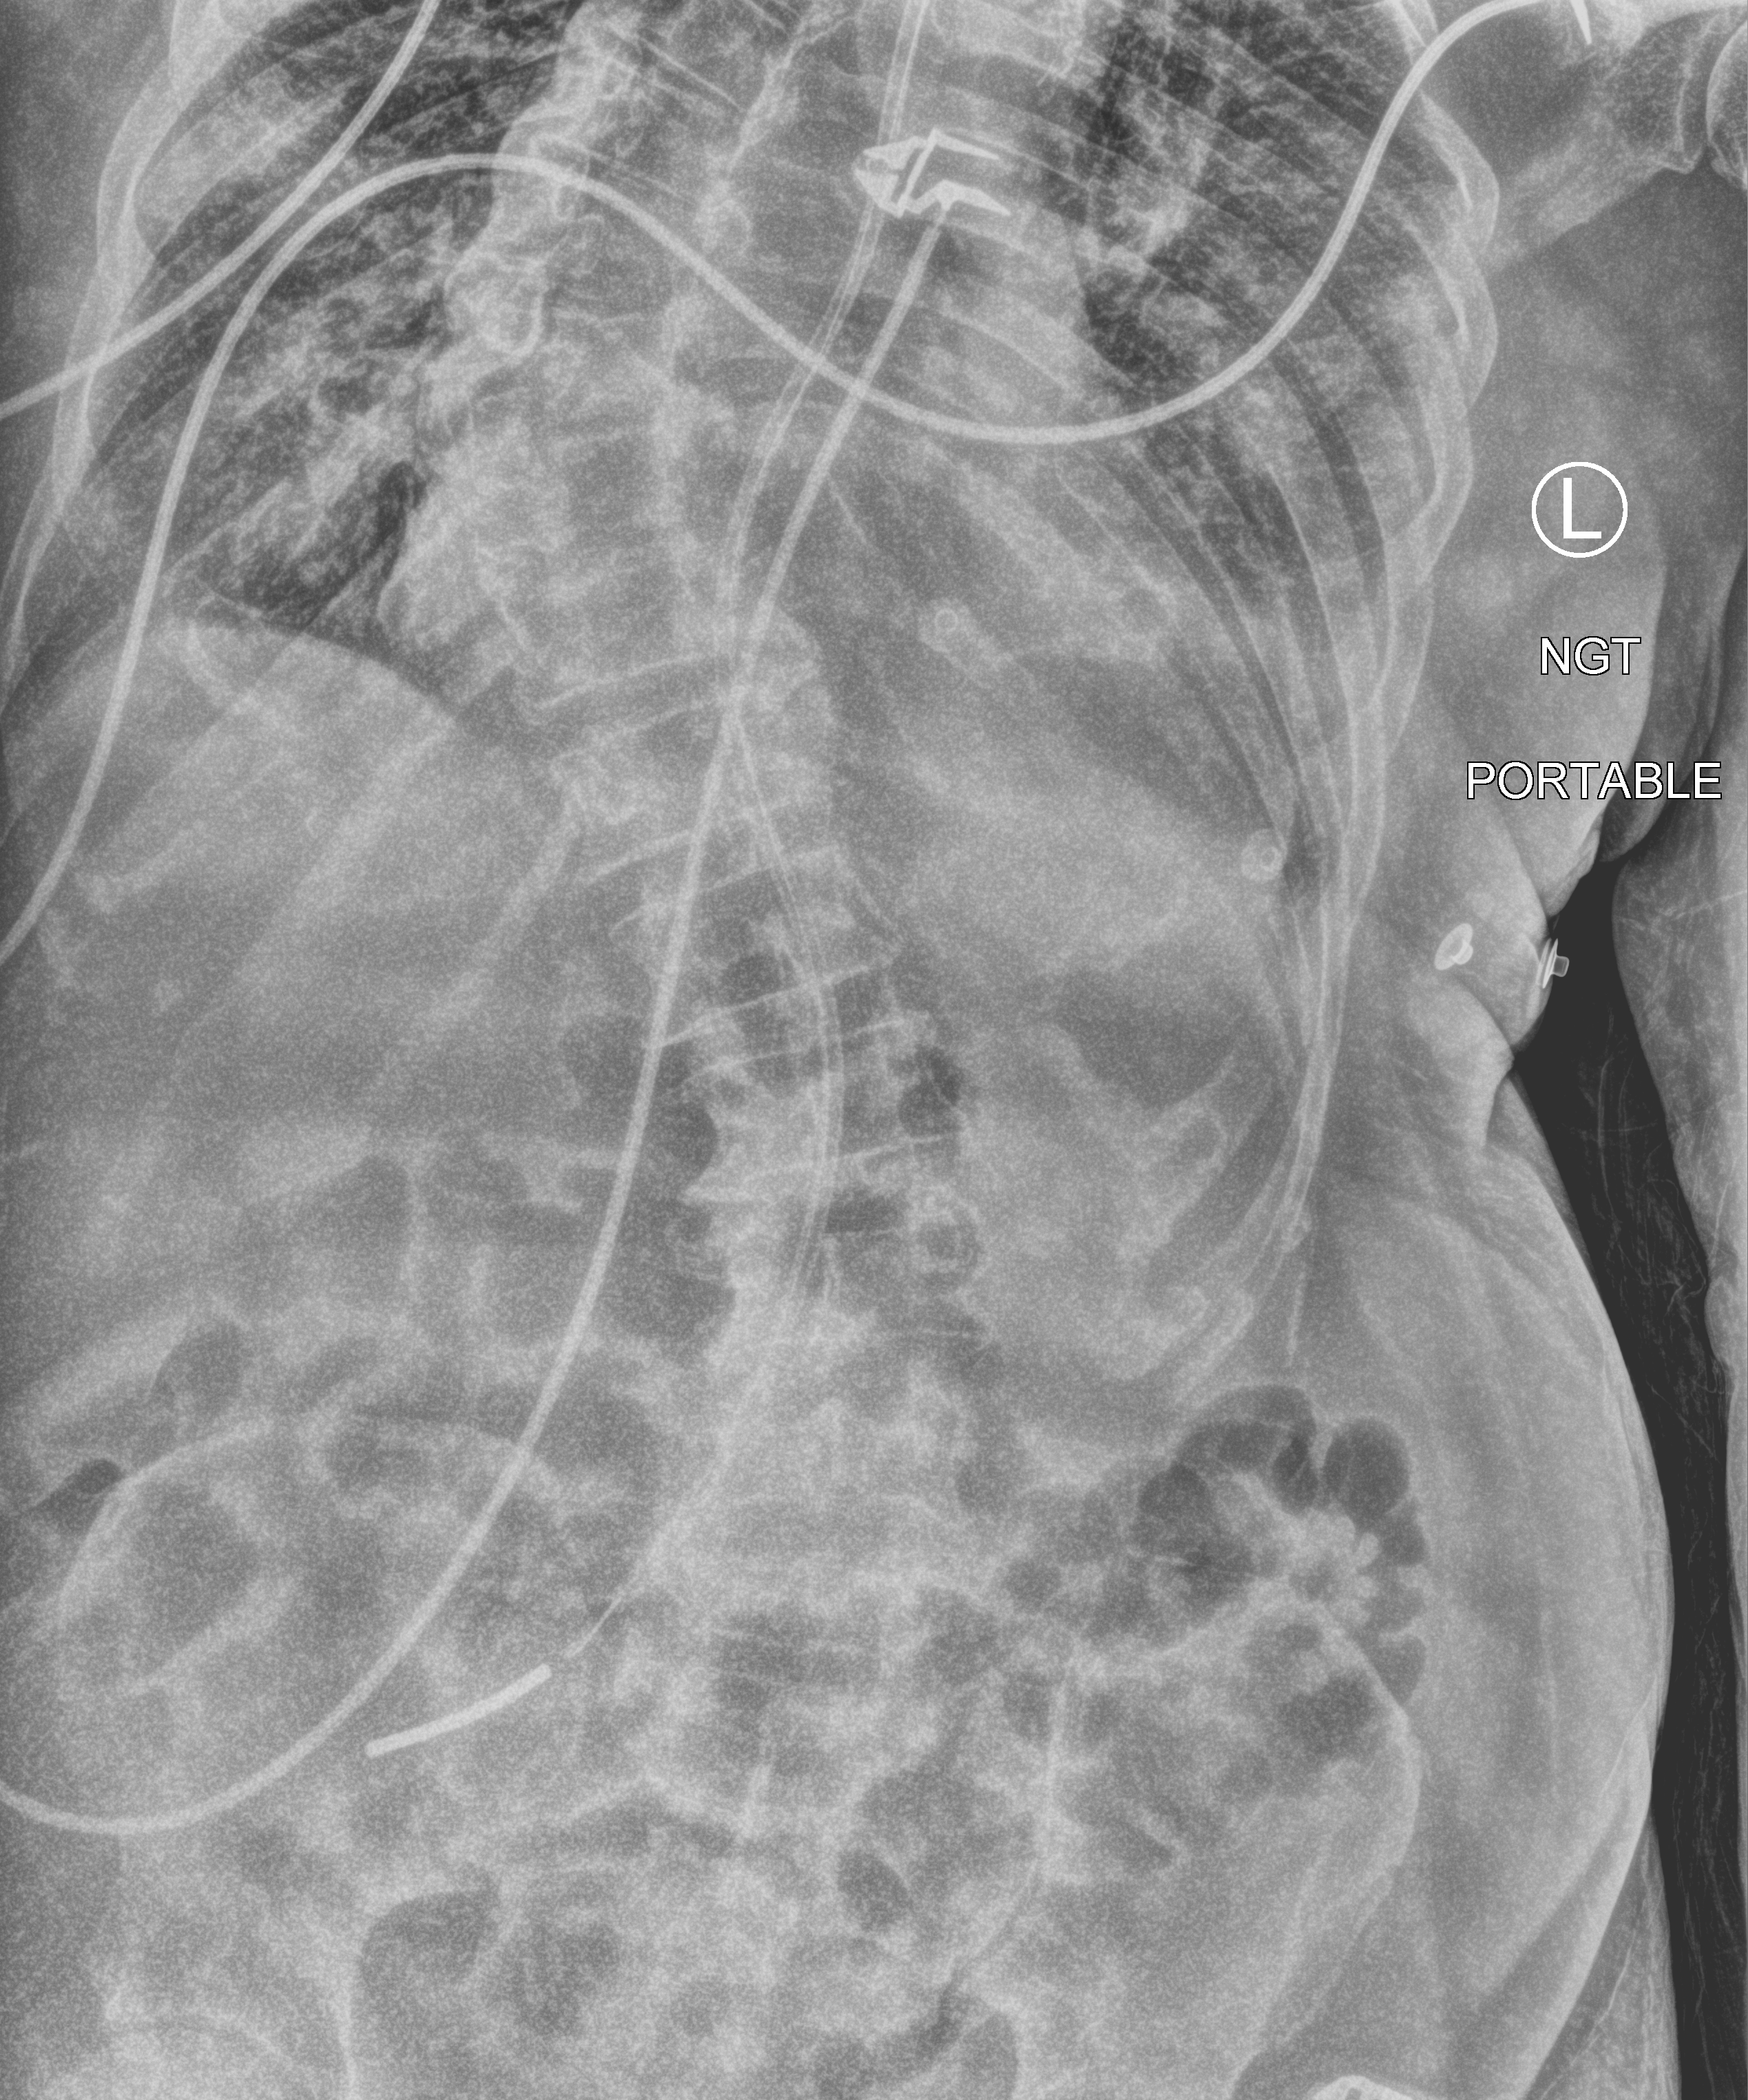
Bedside chest radiograph (computed radiography), anteroposterior (AP) projection. Patient hospitalised with COVID-19; male, aged 75–90 years.
Hospital-stay facts (about this admission, not read from this image; timing relative to this image not recorded):
- admitted to intensive care during this hospital stay: no